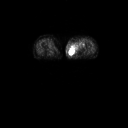
FDG PET of an extremity soft-tissue mass (from a PET/CT study), one axial slice; slice 17 of 91 in the series (ordered by position); 3.27 mm slice thickness; 128 × 128 image matrix, field of view 700 × 700 mm. Patient: female, 74 years. Case-level facts recorded for this patient, not image findings: histological type: pleomorphic leiomyosarcoma; grade: high; site of the primary tumour: left thigh.
Structures marked on this image (expert contour drawn on MRI and transferred to this co-registered scan by the dataset authors):
- gross tumour volume including surrounding oedema: box from (x=69, y=41) to (x=85, y=55) px
- gross tumour volume (mass): (x=69, y=47)–(x=76, y=55)